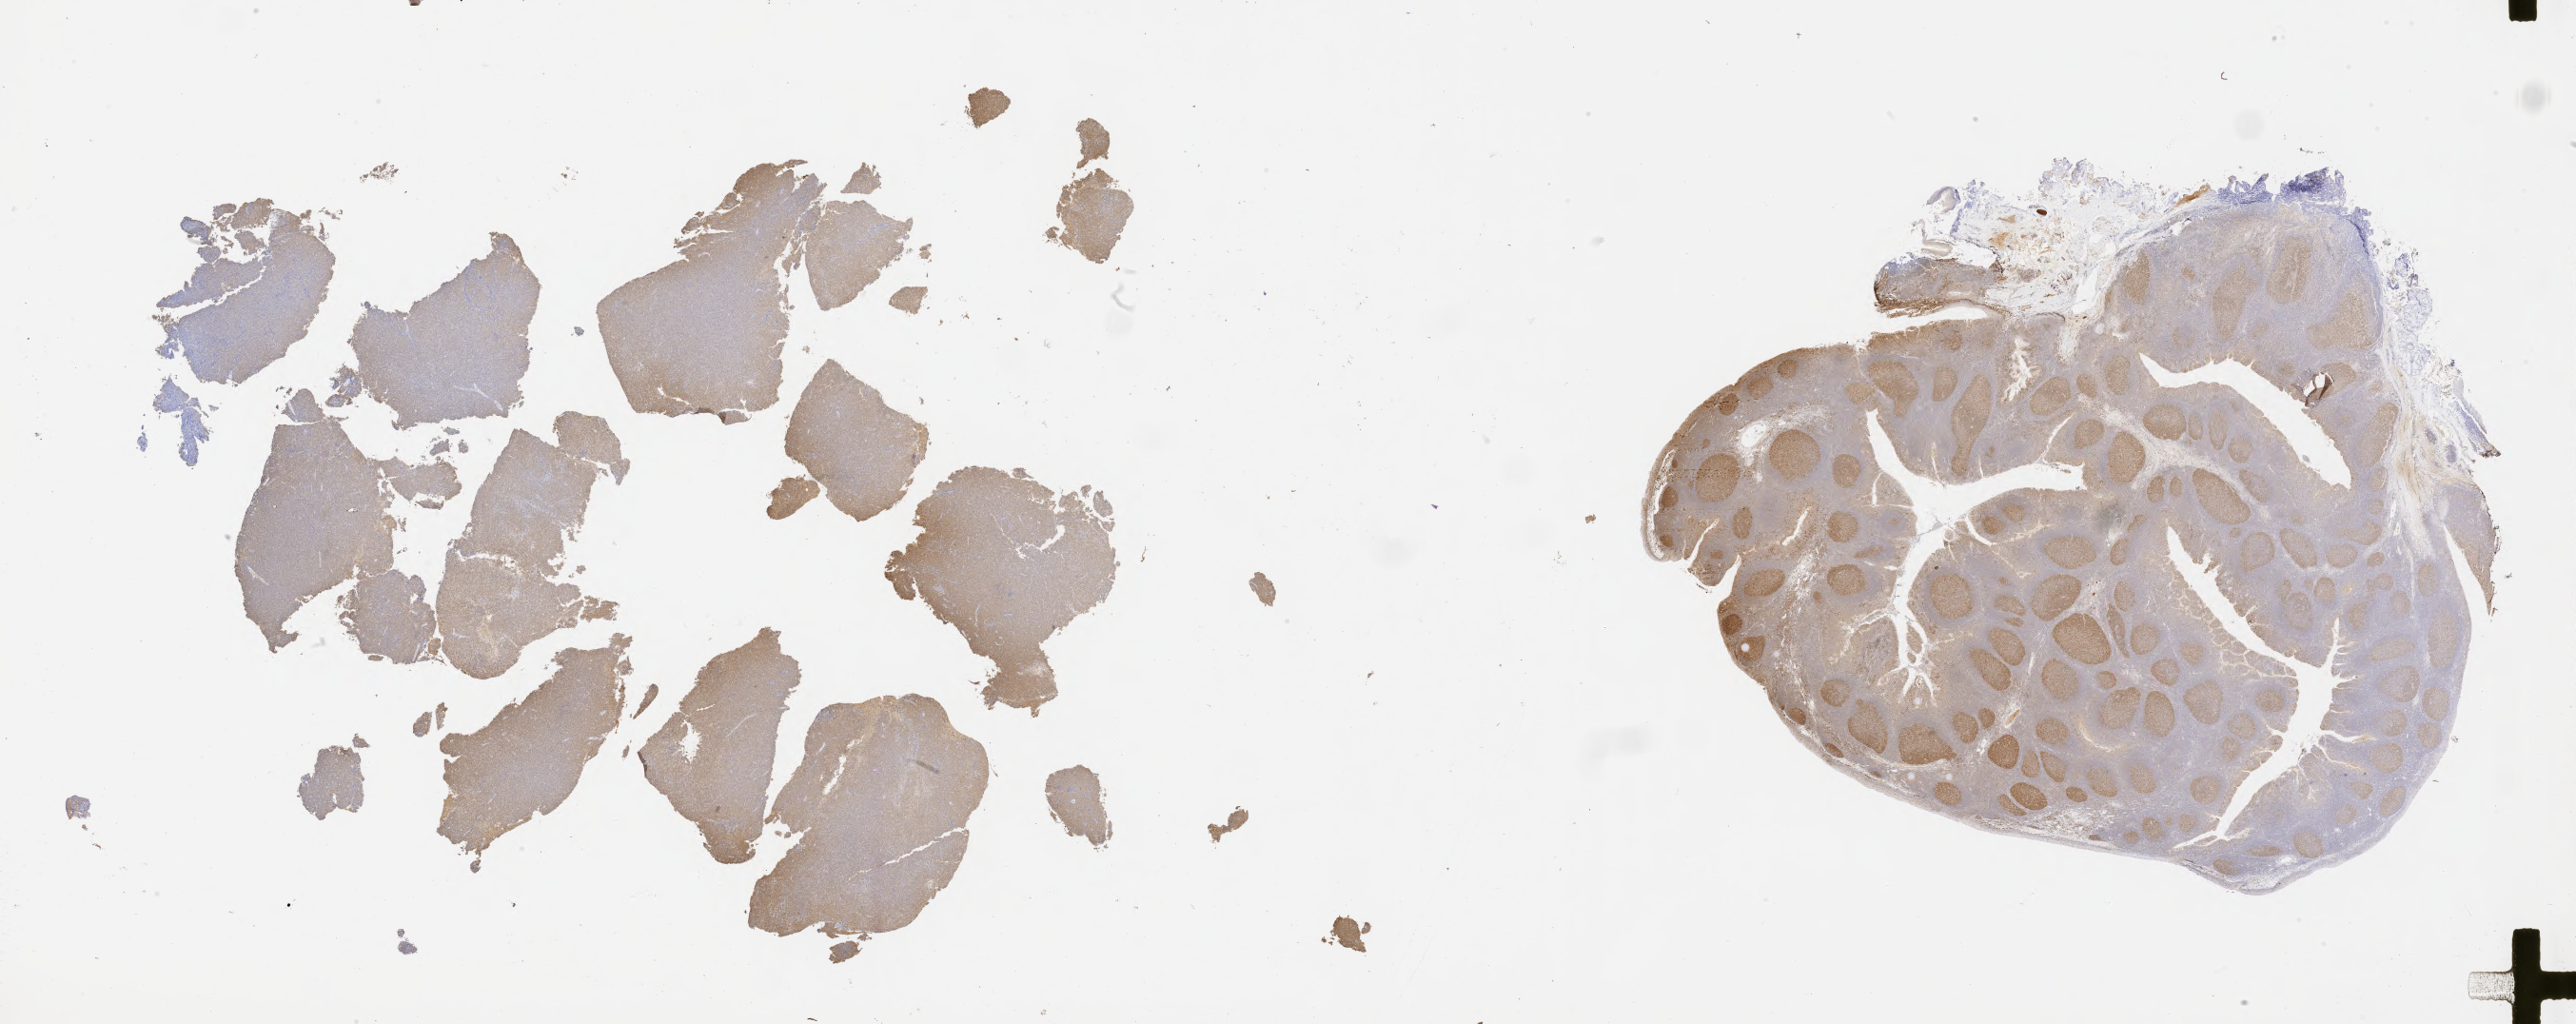
IHC for BCL6, whole-slide image — whole scanned area (about 43.8 x 17.4 mm) shown as a low-resolution overview. Specimen: tumor tissue. Anatomic site: lymph node. Patient: female, aged 50.
Diagnosis: Diffuse large B-cell lymphoma, NOS.